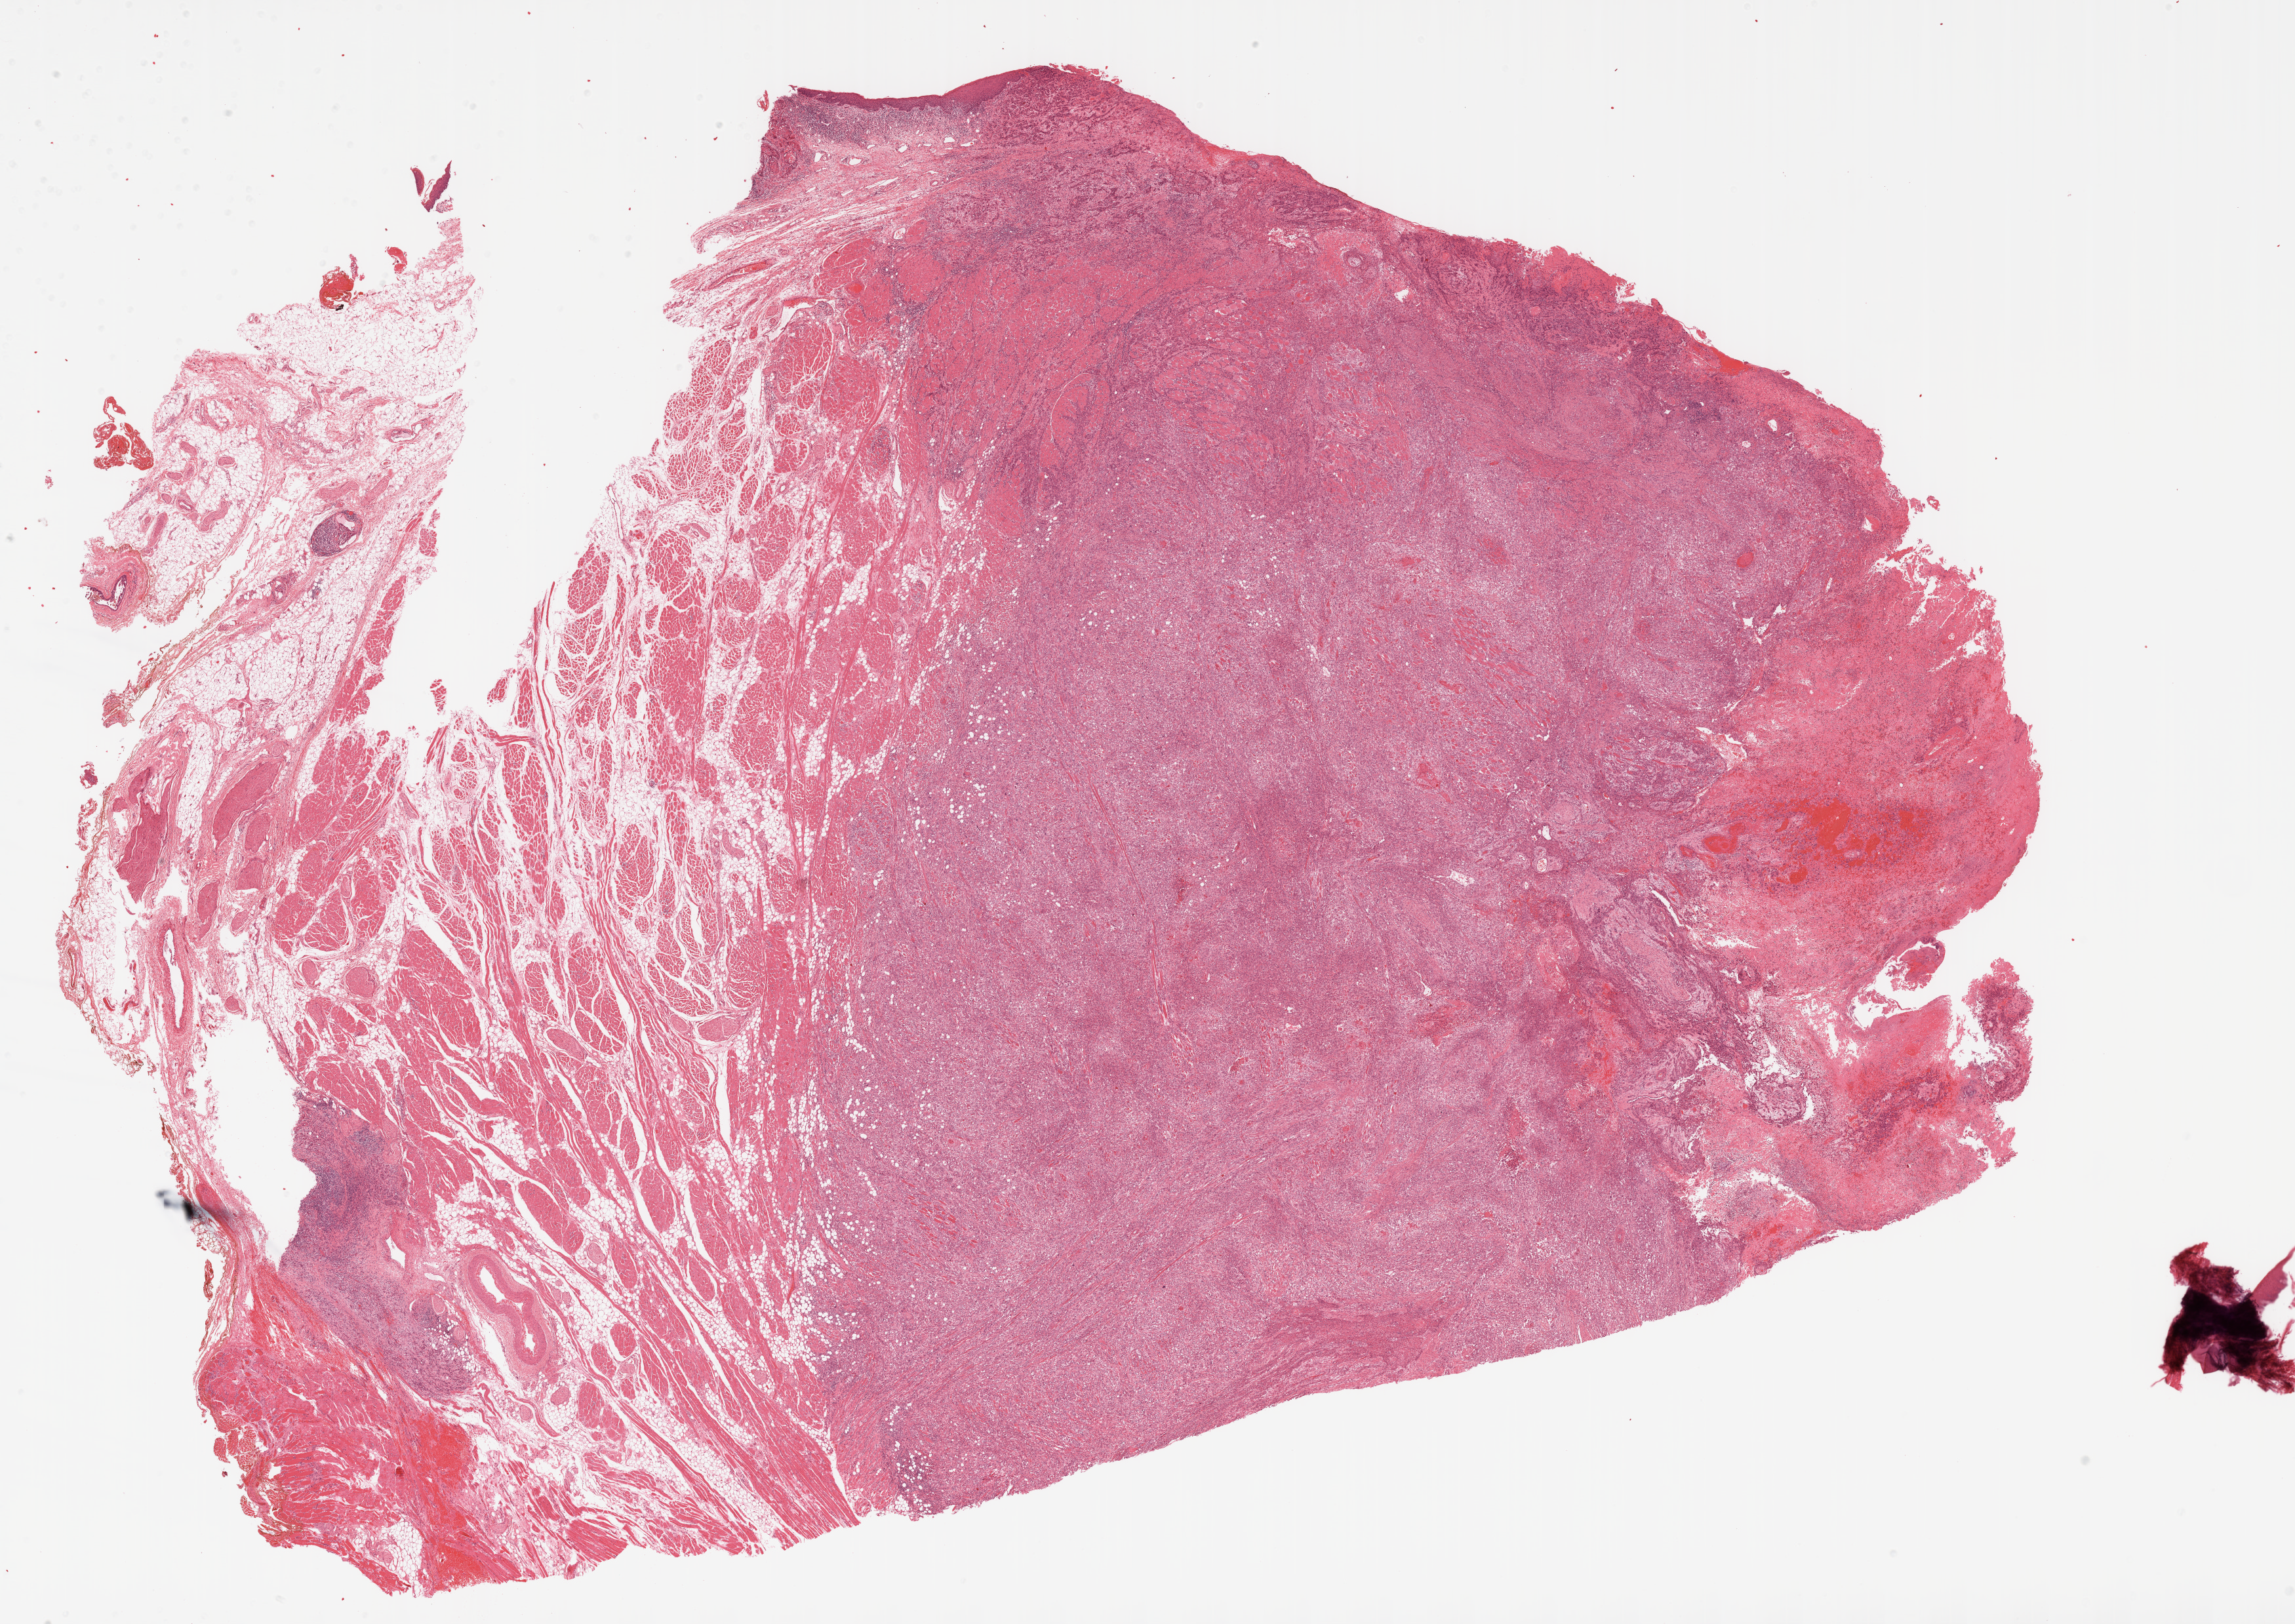
Digitized H&E tissue section (whole slide), shown as a low-resolution overview of the whole scanned area (about 28.1 x 19.9 mm, slide scanned at 20x); FFPE section; sample: primary tumour, head and neck. Patient: female, age at initial diagnosis 69 years. Histologic grade: G3 (poorly differentiated).
TNM: T3 N2b. Laterality: right. Pathologic diagnosis: Squamous cell carcinoma, NOS (tongue, NOS). AJCC pathologic stage: IVA (6th edition).